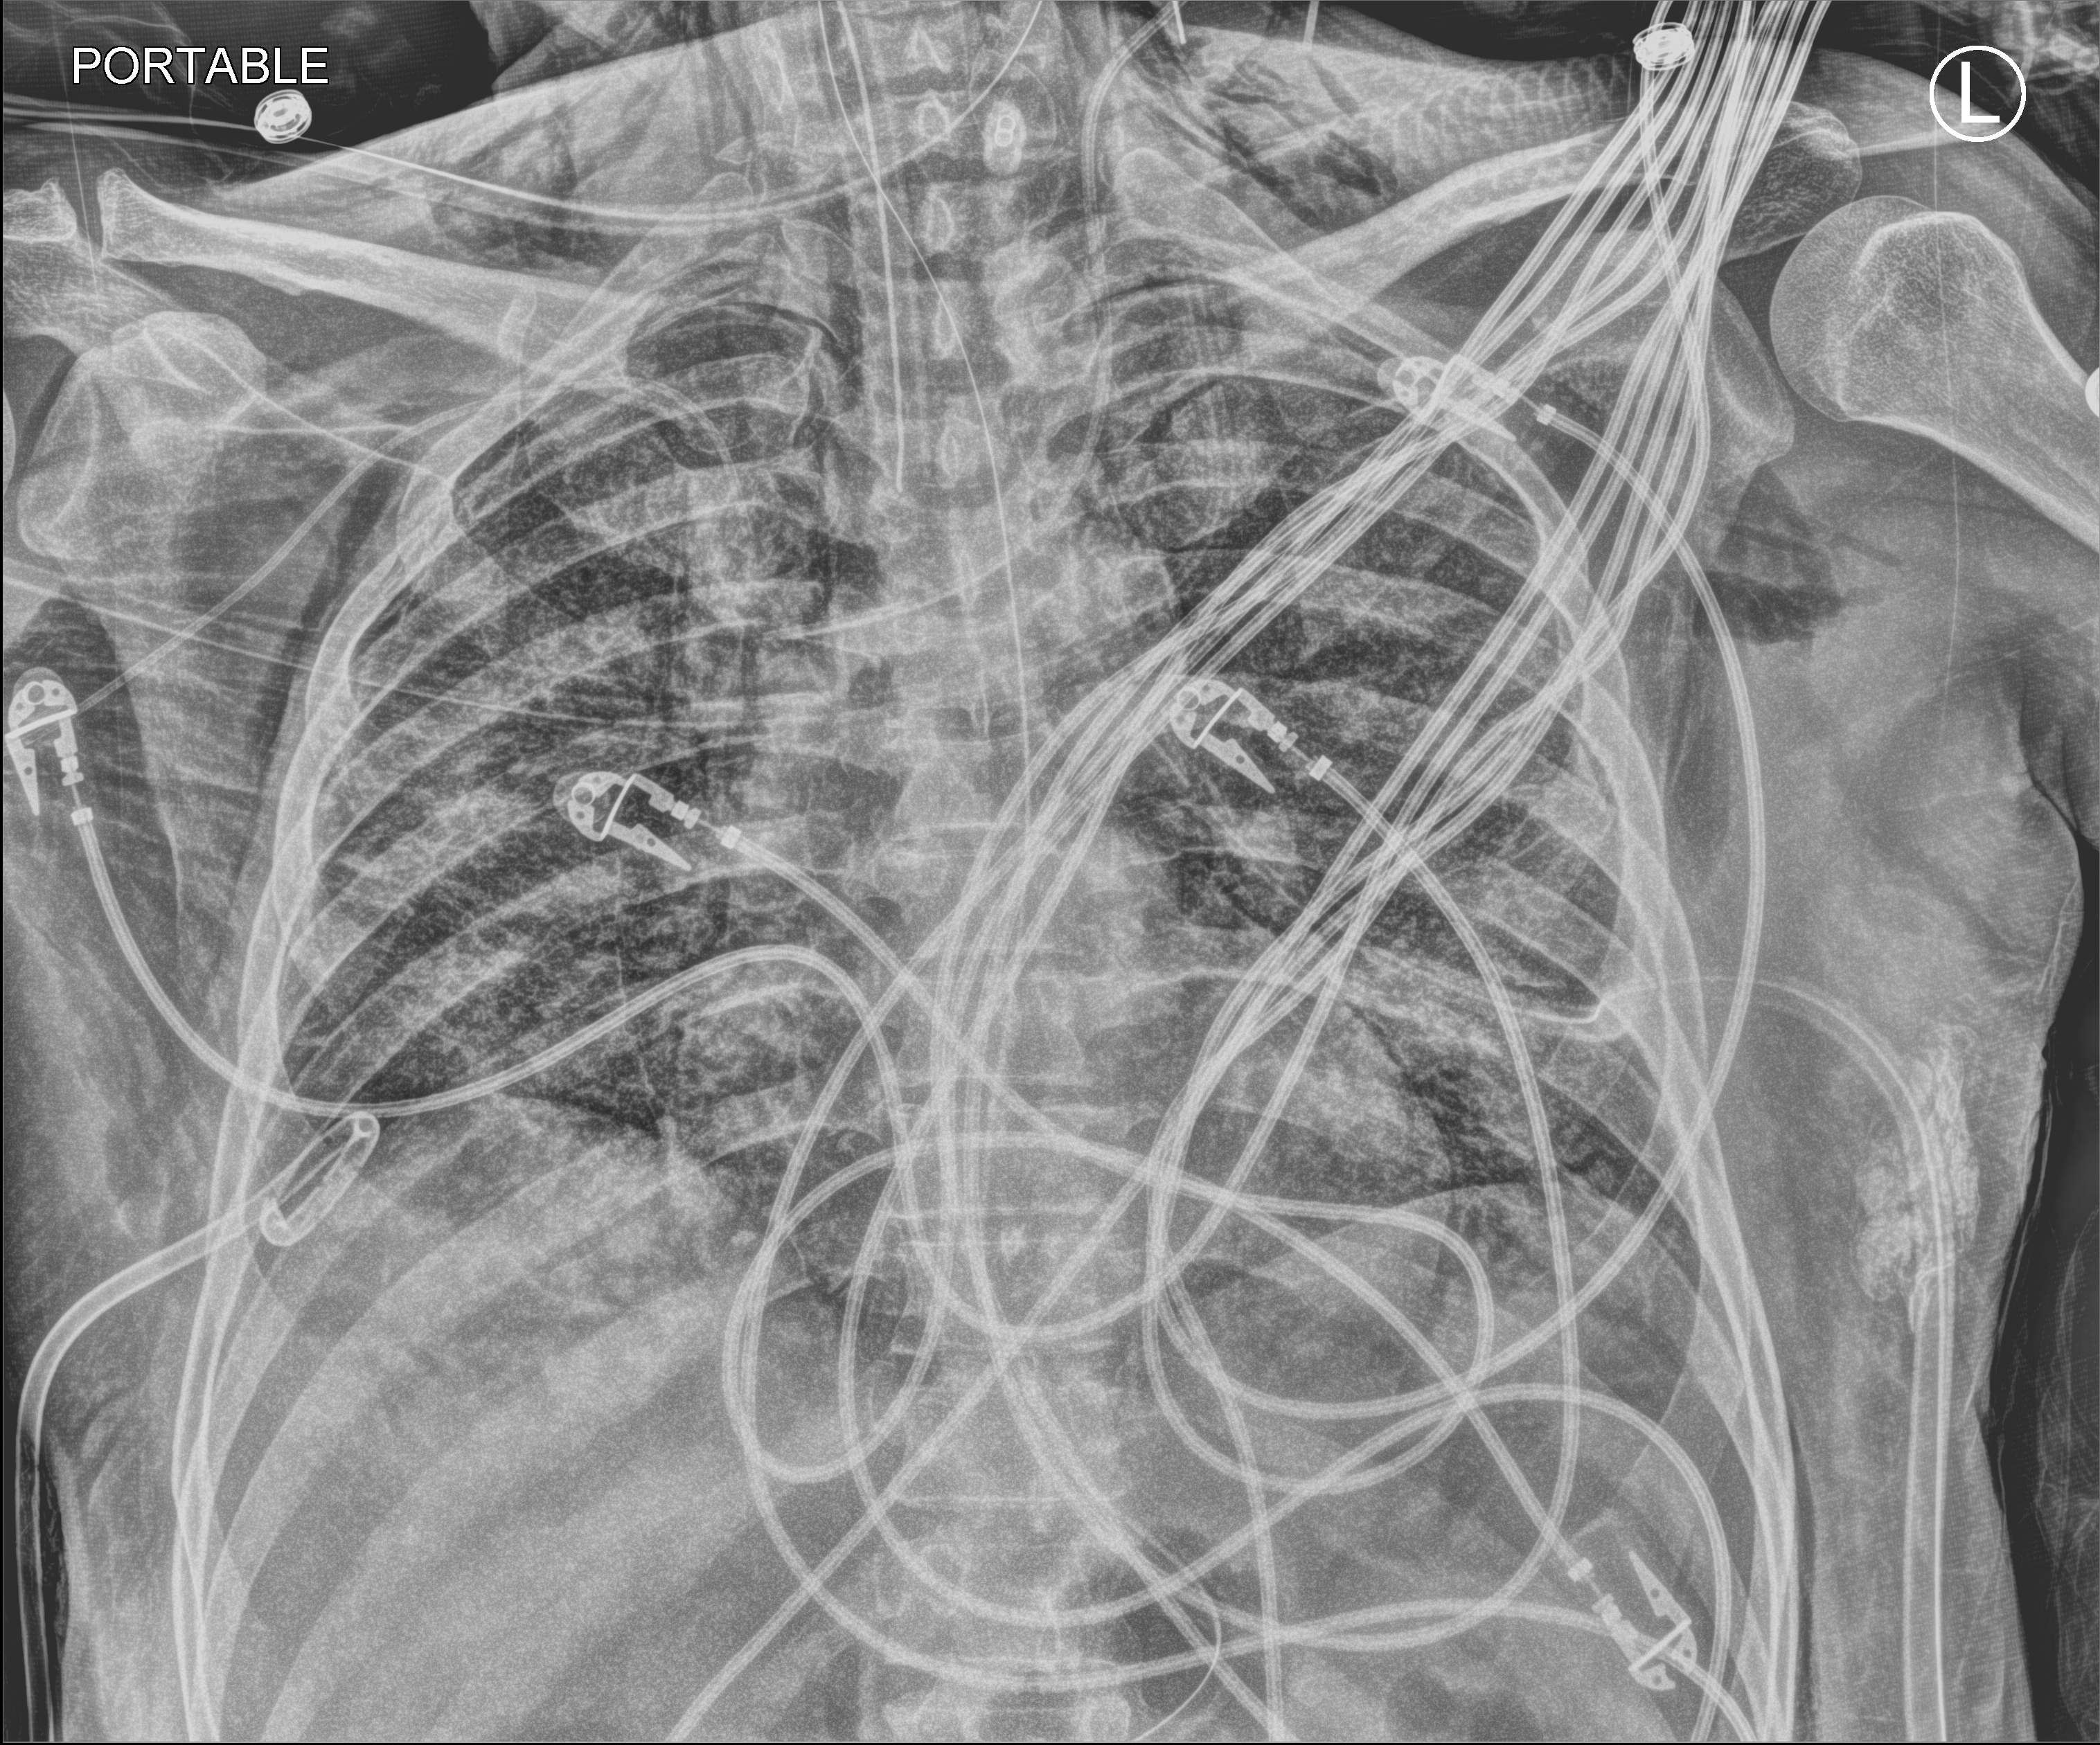
Chest X-ray (portable). Patient hospitalised with COVID-19; male, aged 18–59 years.
Admission-level facts for this patient (not findings on this image; timing relative to this image not recorded):
- admitted to intensive care during this hospital stay: yes